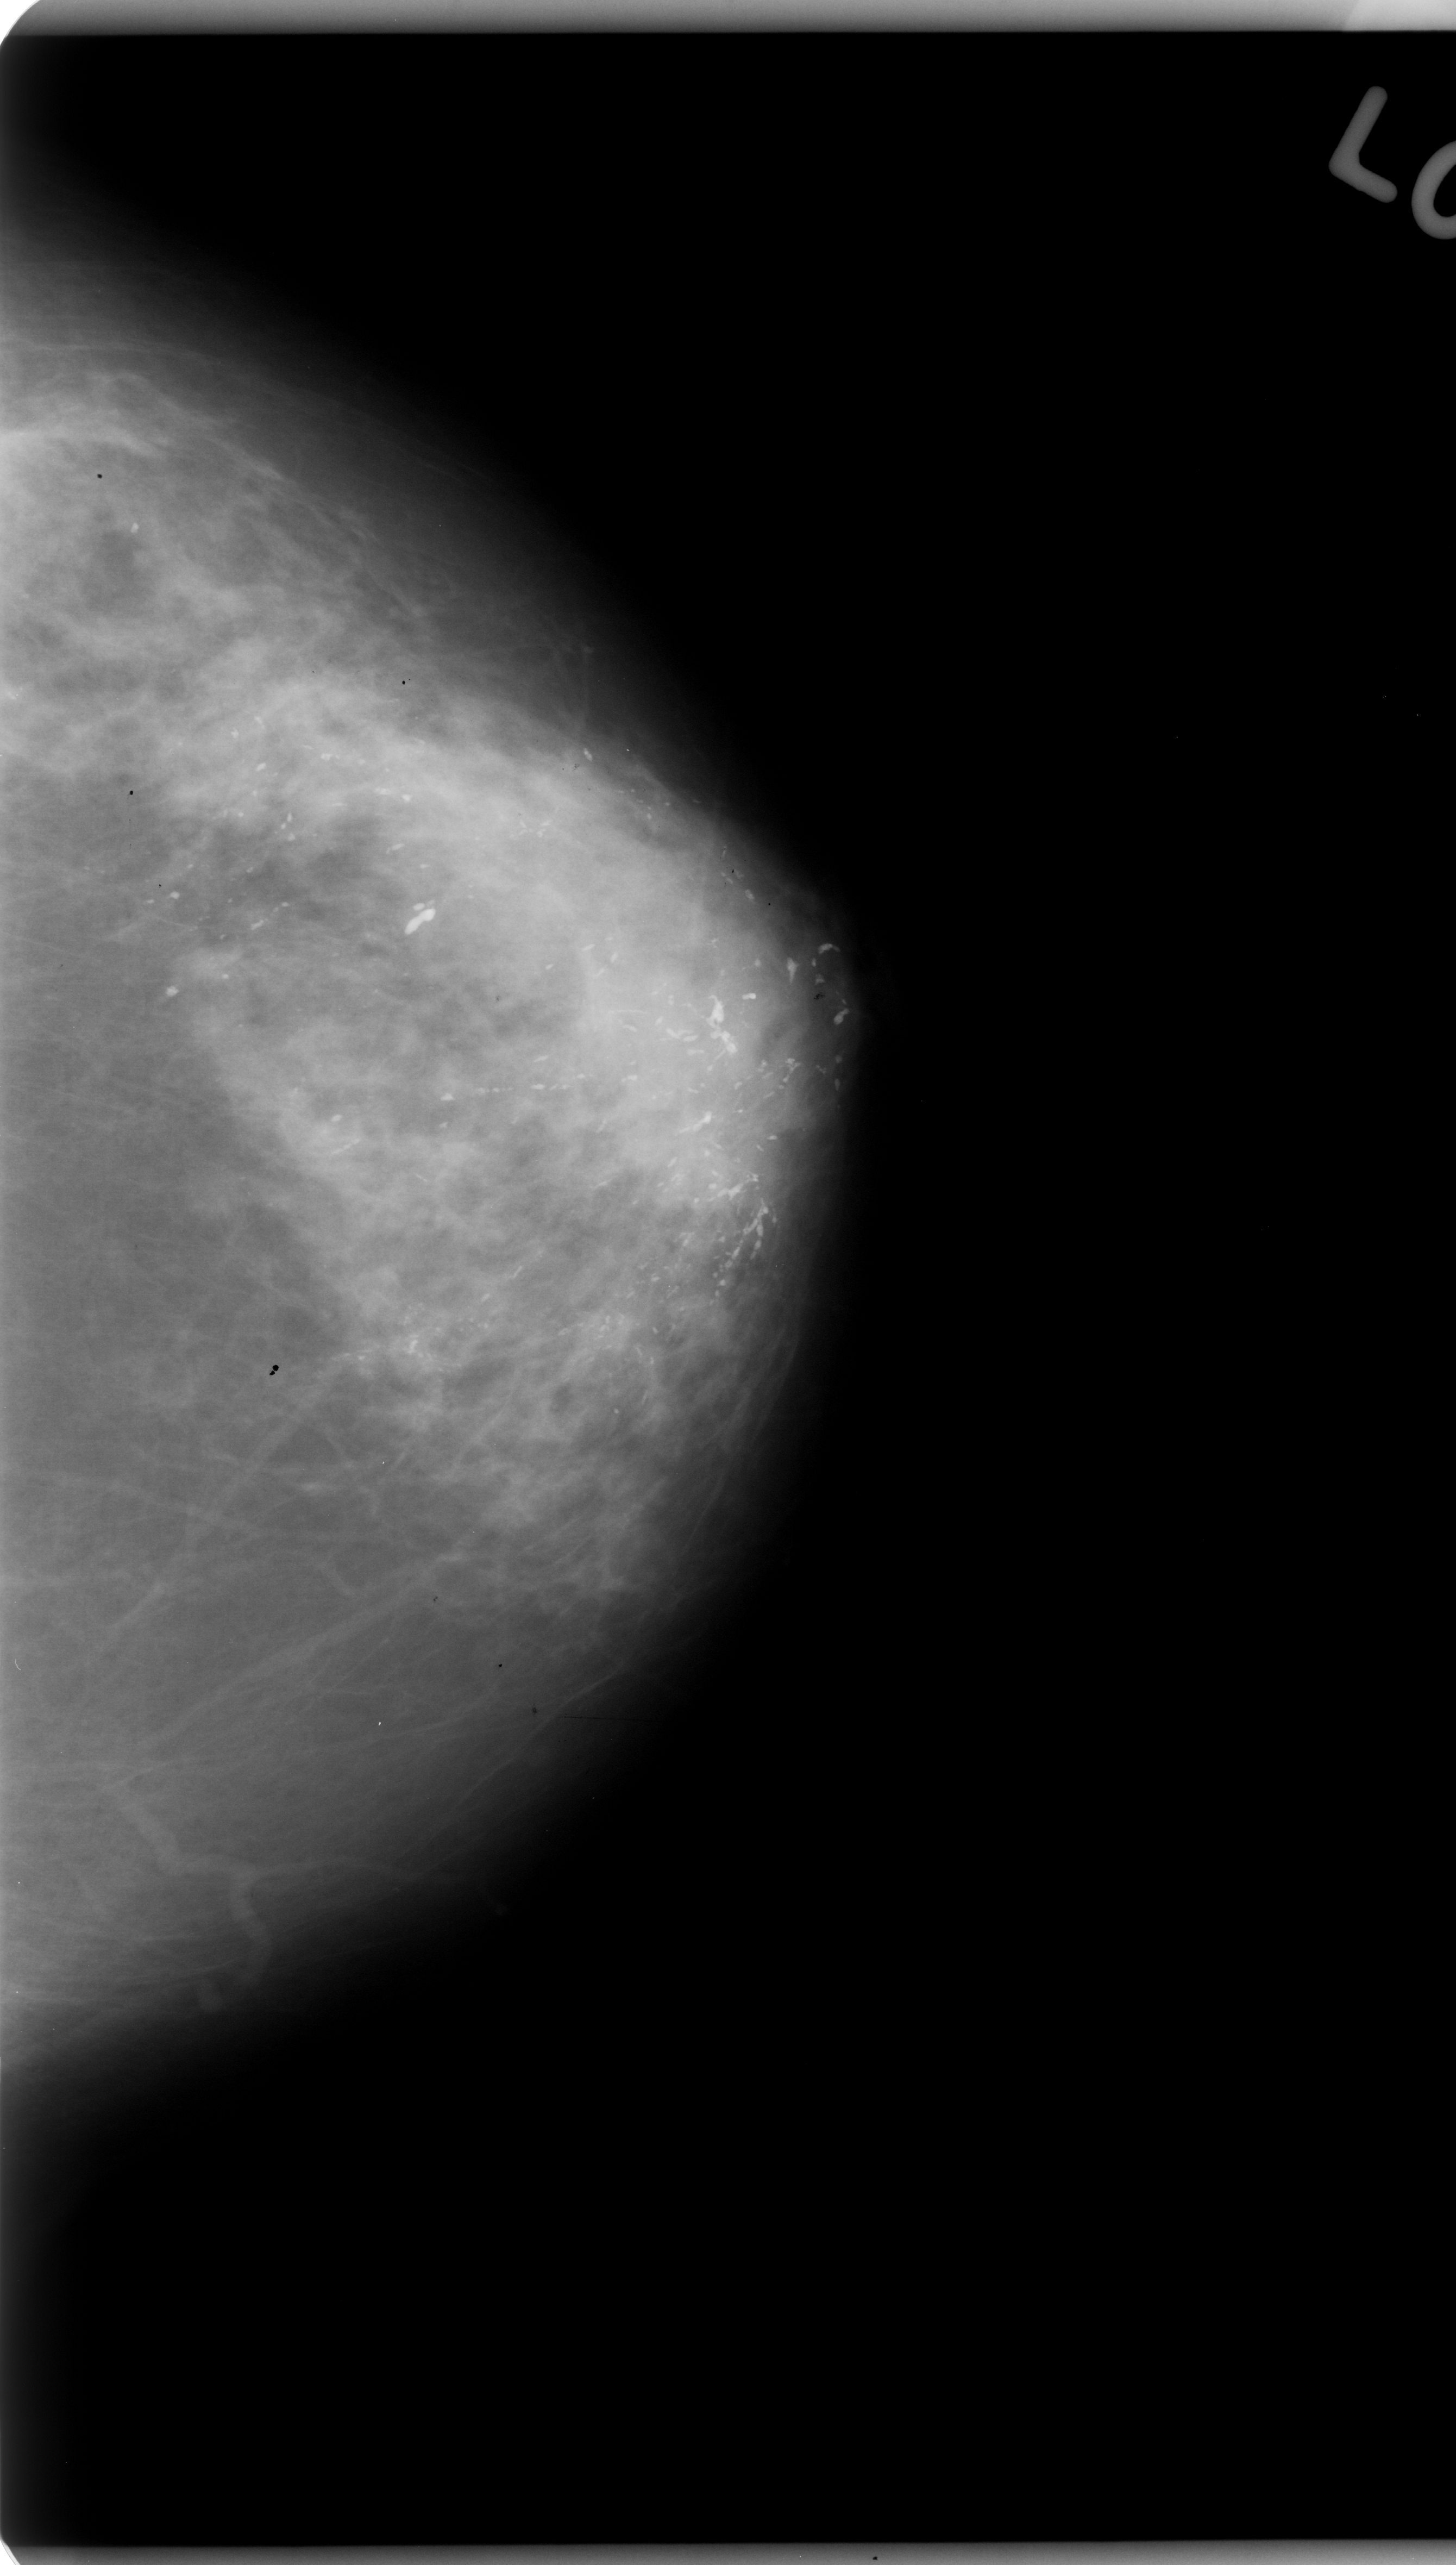
Digitized screen-film mammogram; left breast; CC view; BI-RADS breast density category 3 (scale 1–4); 1456 × 2565 image matrix.
Marked abnormalities (boxes around the expert regions of interest):
- calcifications, morphology fine linear branching, distribution regional; BI-RADS assessment category 5; pathology result (as recorded, not read from the image): malignant: box from (x=56, y=452) to (x=853, y=1740) px